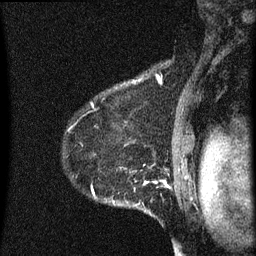
Breast MRI (dynamic contrast-enhanced), one sagittal slice; slice 50 of 60 in the series (ordered by position); dynamic contrast-enhanced series, image 2 of 3 at this slice position (ordered by acquisition); 1.5 T; TE 4.2 ms, TR 8 ms; 2 mm slice thickness; 256 × 256 image matrix. Patient: female, 55 years.
Annotated regions visible in this slice (semi-automatic segmentation, software-assisted and operator-edited):
- analysis volume of interest (the breast-tissue region the enhancement analysis was run in; not a lesion): bounding box [x1, y1, x2, y2] px = [64, 156, 145, 211]
- tumour enhancement mask (voxels above the 70 % enhancement threshold inside the analysis volume of interest): [93, 184, 145, 207]